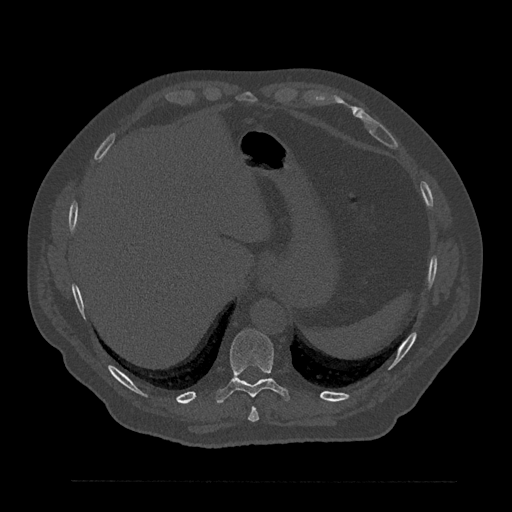
CT including the spine, one axial slice. Position 351 of 797 along the scan axis. 120 kVp. Bone window (W 1800 / L 400 HU). 0.5 mm slice thickness. 512 × 512 image matrix, field of view 430 × 430 mm. Male patient, age 61 years. Case-level facts recorded for this patient, not image findings: primary cancer: prostate.
Outlined on this slice (semi-automatic segmentation, software-assisted and operator-edited):
- T10 vertebra: bounding box (x1, y1, x2, y2) in pixels: (216, 329, 290, 403)
- T9 vertebra: (248, 406, 259, 422)